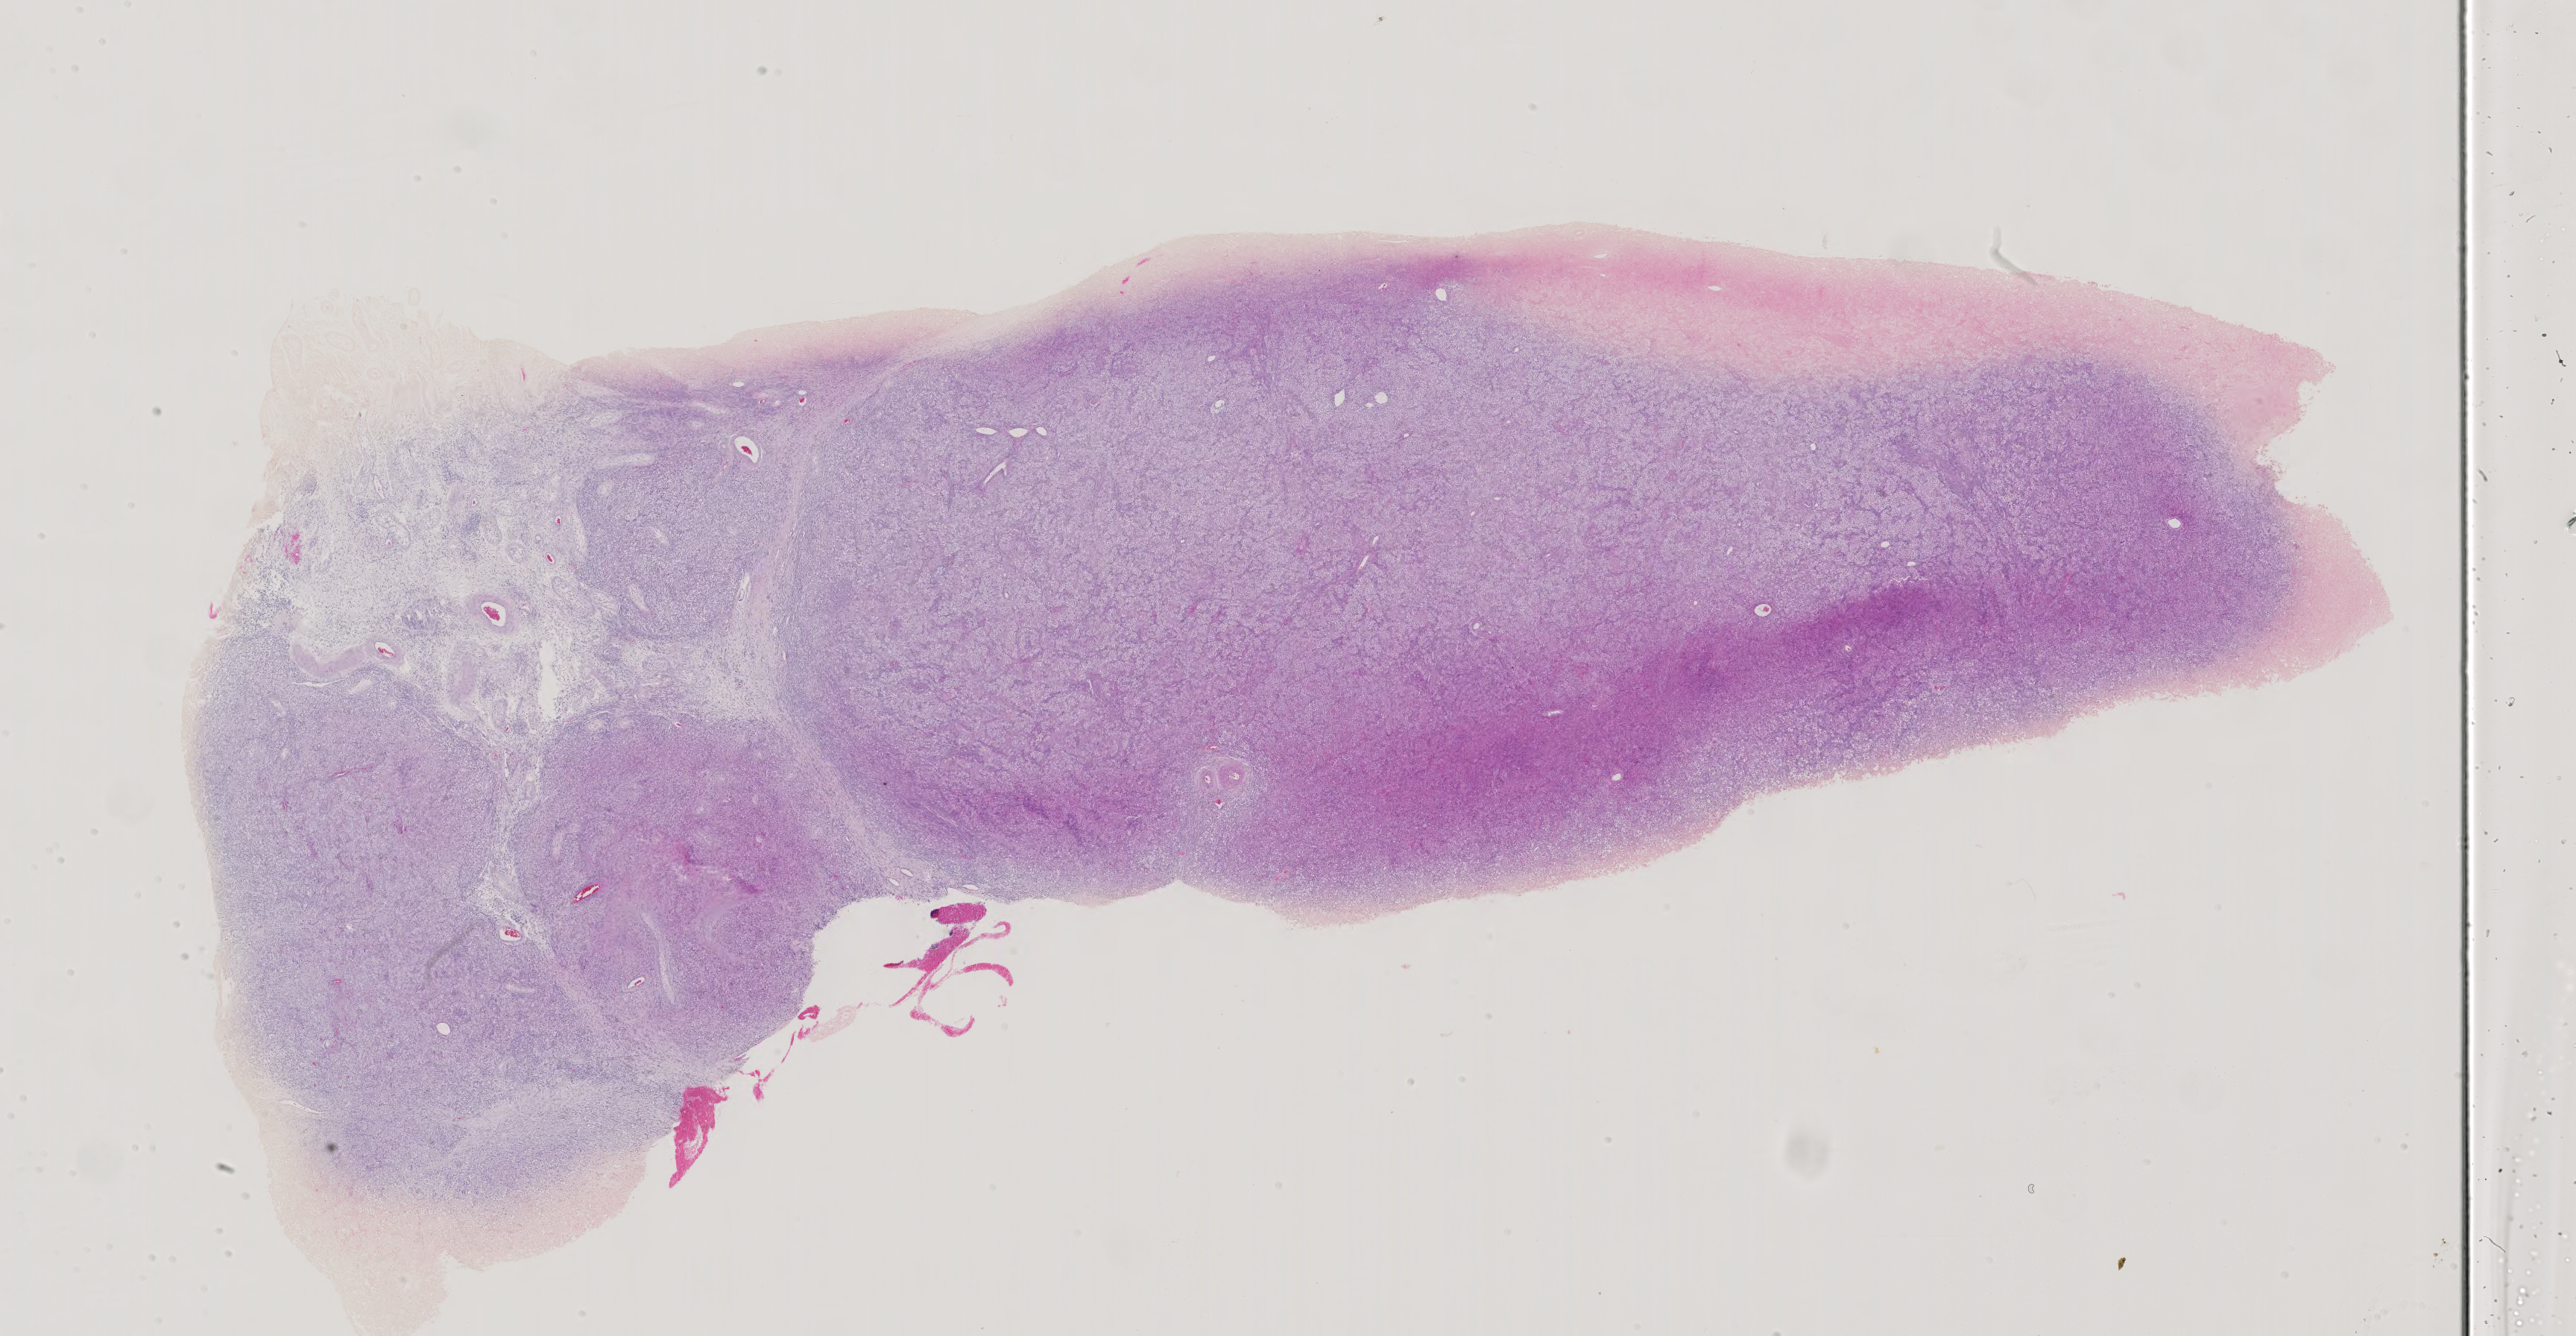
Hematoxylin and eosin (H&E) stained whole-slide image — a low-resolution overview of the entire scanned area, about 25.2 x 13.1 mm (slide scanned at 40x); formalin-fixed paraffin-embedded (FFPE) diagnostic section; testis, primary tumour sample. Male patient; age at initial diagnosis 32 years.
Laterality: left. Pathologic diagnosis: Seminoma, NOS. TNM: T1 N0 M0. AJCC pathologic stage: I (4th edition).